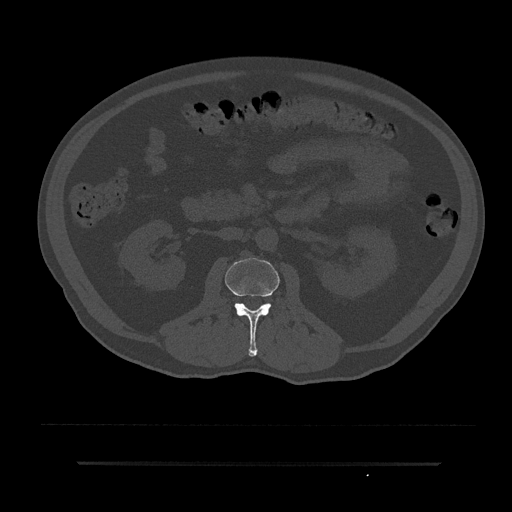
CT including the spine, one axial slice; position 66 of 797 along the scan axis; reconstruction kernel Br40s/3; 120 kVp; bone window (W 1800 / L 400 HU); 0.5 mm slice thickness; 512 × 512 image matrix, field of view 464 × 464 mm. Patient: male, 59 years. Case-level facts recorded for this patient, not image findings: primary cancer: bile ducts.
Outlined on this slice (semi-automatic segmentation, software-assisted and operator-edited):
- L2 vertebra: bounding box (x1, y1, x2, y2) in pixels: (225, 258, 279, 357)